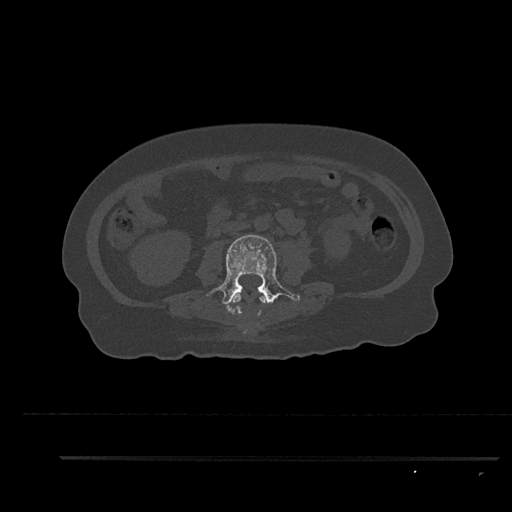
CT including the spine, one axial slice; slice 101 of 797 in the series (ordered by position); reconstruction kernel Br40s/3; bone window (W 1800 / L 400 HU); 0.5 mm slice thickness; 512 × 512 image matrix, field of view 408 × 408 mm. Patient: female, 44 years. From the clinical record (not read from this slice): primary cancer: renal.
Annotated regions visible in this slice (semi-automatic segmentation, software-assisted and operator-edited):
- L2 vertebra: box from (x=231, y=294) to (x=265, y=316) px
- L3 vertebra: (x=206, y=235)–(x=300, y=315)